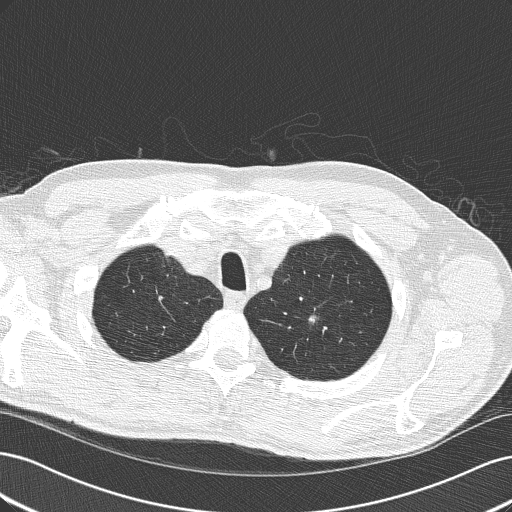
Low-dose screening chest CT, one axial slice; position 156 of 189 along the scan axis; reconstruction kernel B50f; 120 kVp; lung window (W 1500 / L -600 HU); 512 × 512 image matrix, field of view 360 × 360 mm.
Outlined on this slice (expert manual segmentation):
- lesion 1 (tumor, upper lobe of left lung): bounding box (x1, y1, x2, y2) in pixels: (308, 310, 327, 336)